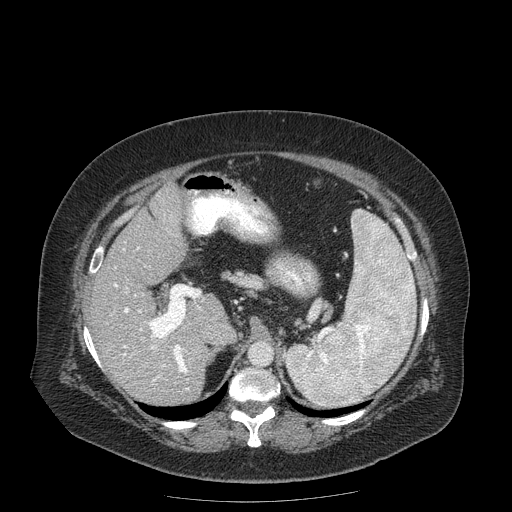
Contrast-enhanced abdominal CT (liver protocol), one axial slice. Position 111 of 204 along the scan axis. 120 kVp. Soft-tissue window (W 400 / L 40 HU). 2.5 mm slice thickness. 512 × 512 image matrix, field of view 440 × 440 mm. Case-level facts recorded for this patient, not image findings: diagnosis: hepatocellular carcinoma (patient treated with transarterial chemoembolisation; whether this scan precedes or follows treatment is not stated here); TNM stage (as recorded): Stage-IIIB; Child-Pugh class: A; tumour differentiation: well differentiated; tumour nodularity: uninodular.
Annotated regions visible in this slice (semi-automatically segmented with operator editing):
- liver parenchyma outside the tumour (the mass and vessels are separate outlines, so this box may not span the whole liver): box from (x=90, y=184) to (x=232, y=404) px
- liver vessels: (x=113, y=247)–(x=200, y=389)